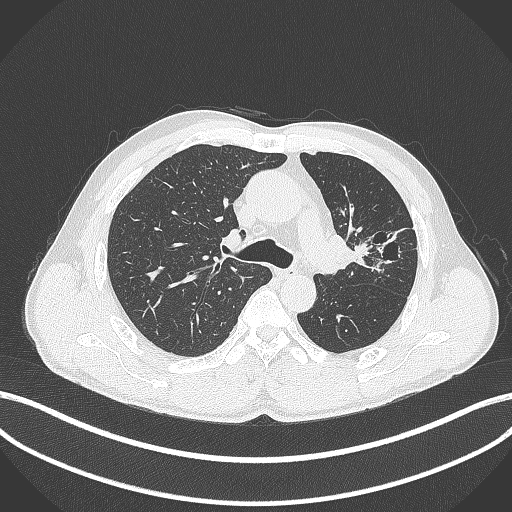
Chest CT, one axial slice; slice 276 of 429 in the series (ordered by position); reconstruction kernel B70f; lung window (W 1500 / L -600 HU); 1 mm slice thickness; 512 × 512 image matrix. Patient: male, 57 years. From the clinical record (not read from this slice): clinical TNM (as recorded): T2b N0 M0.
Outlined on this slice (rectangle marked by the reading radiologist):
- lung tumour (recorded histology: squamous cell carcinoma): bounding box <328,232,381,274> (left, top, right, bottom; pixels)